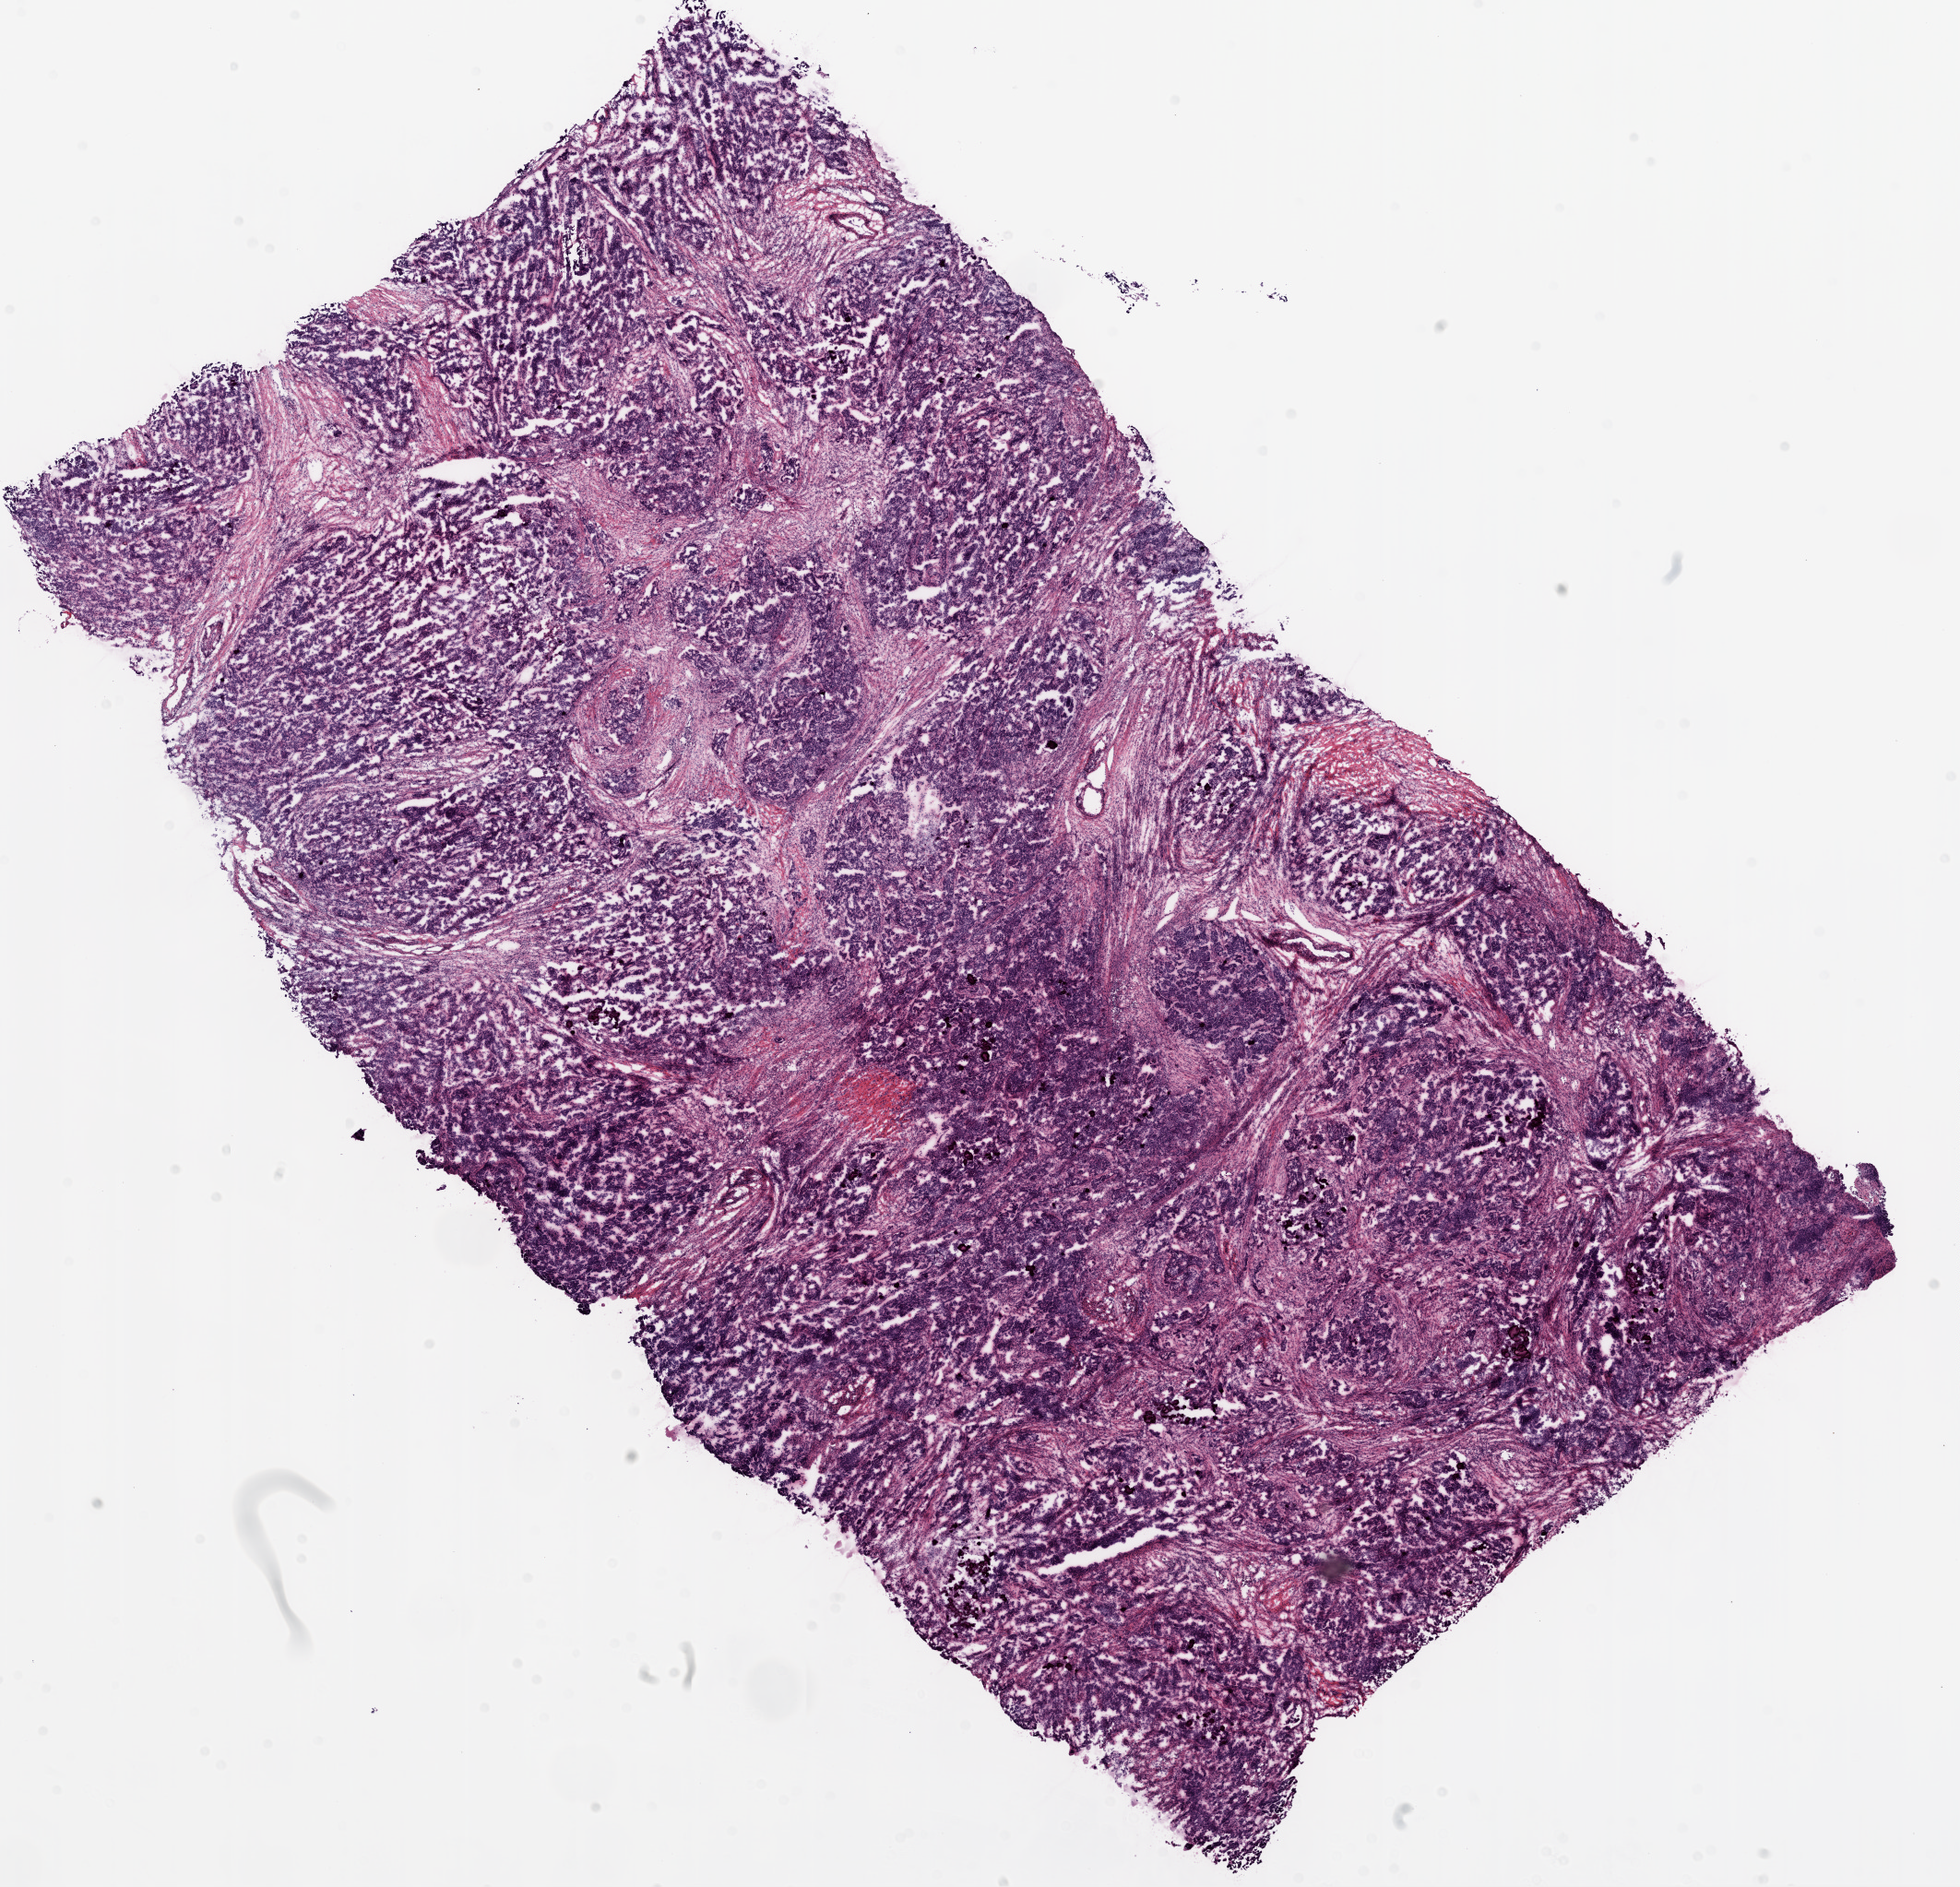
Digitized H&E tissue section (whole slide) — a low-resolution overview of the entire scanned area, about 17.1 x 16.4 mm (slide scanned at 20x); frozen section; primary tumour sample from the ovary. Patient: female, age at initial diagnosis 41 years. Histologic grade: G3 (poorly differentiated). Pathologist review of this section (percent, as recorded): tumour cells 89%, tumour nuclei 90%, normal cells 0%, stromal cells 10%, necrosis 1%.
- FIGO stage: IV
- histologic diagnosis: Serous cystadenocarcinoma, NOS